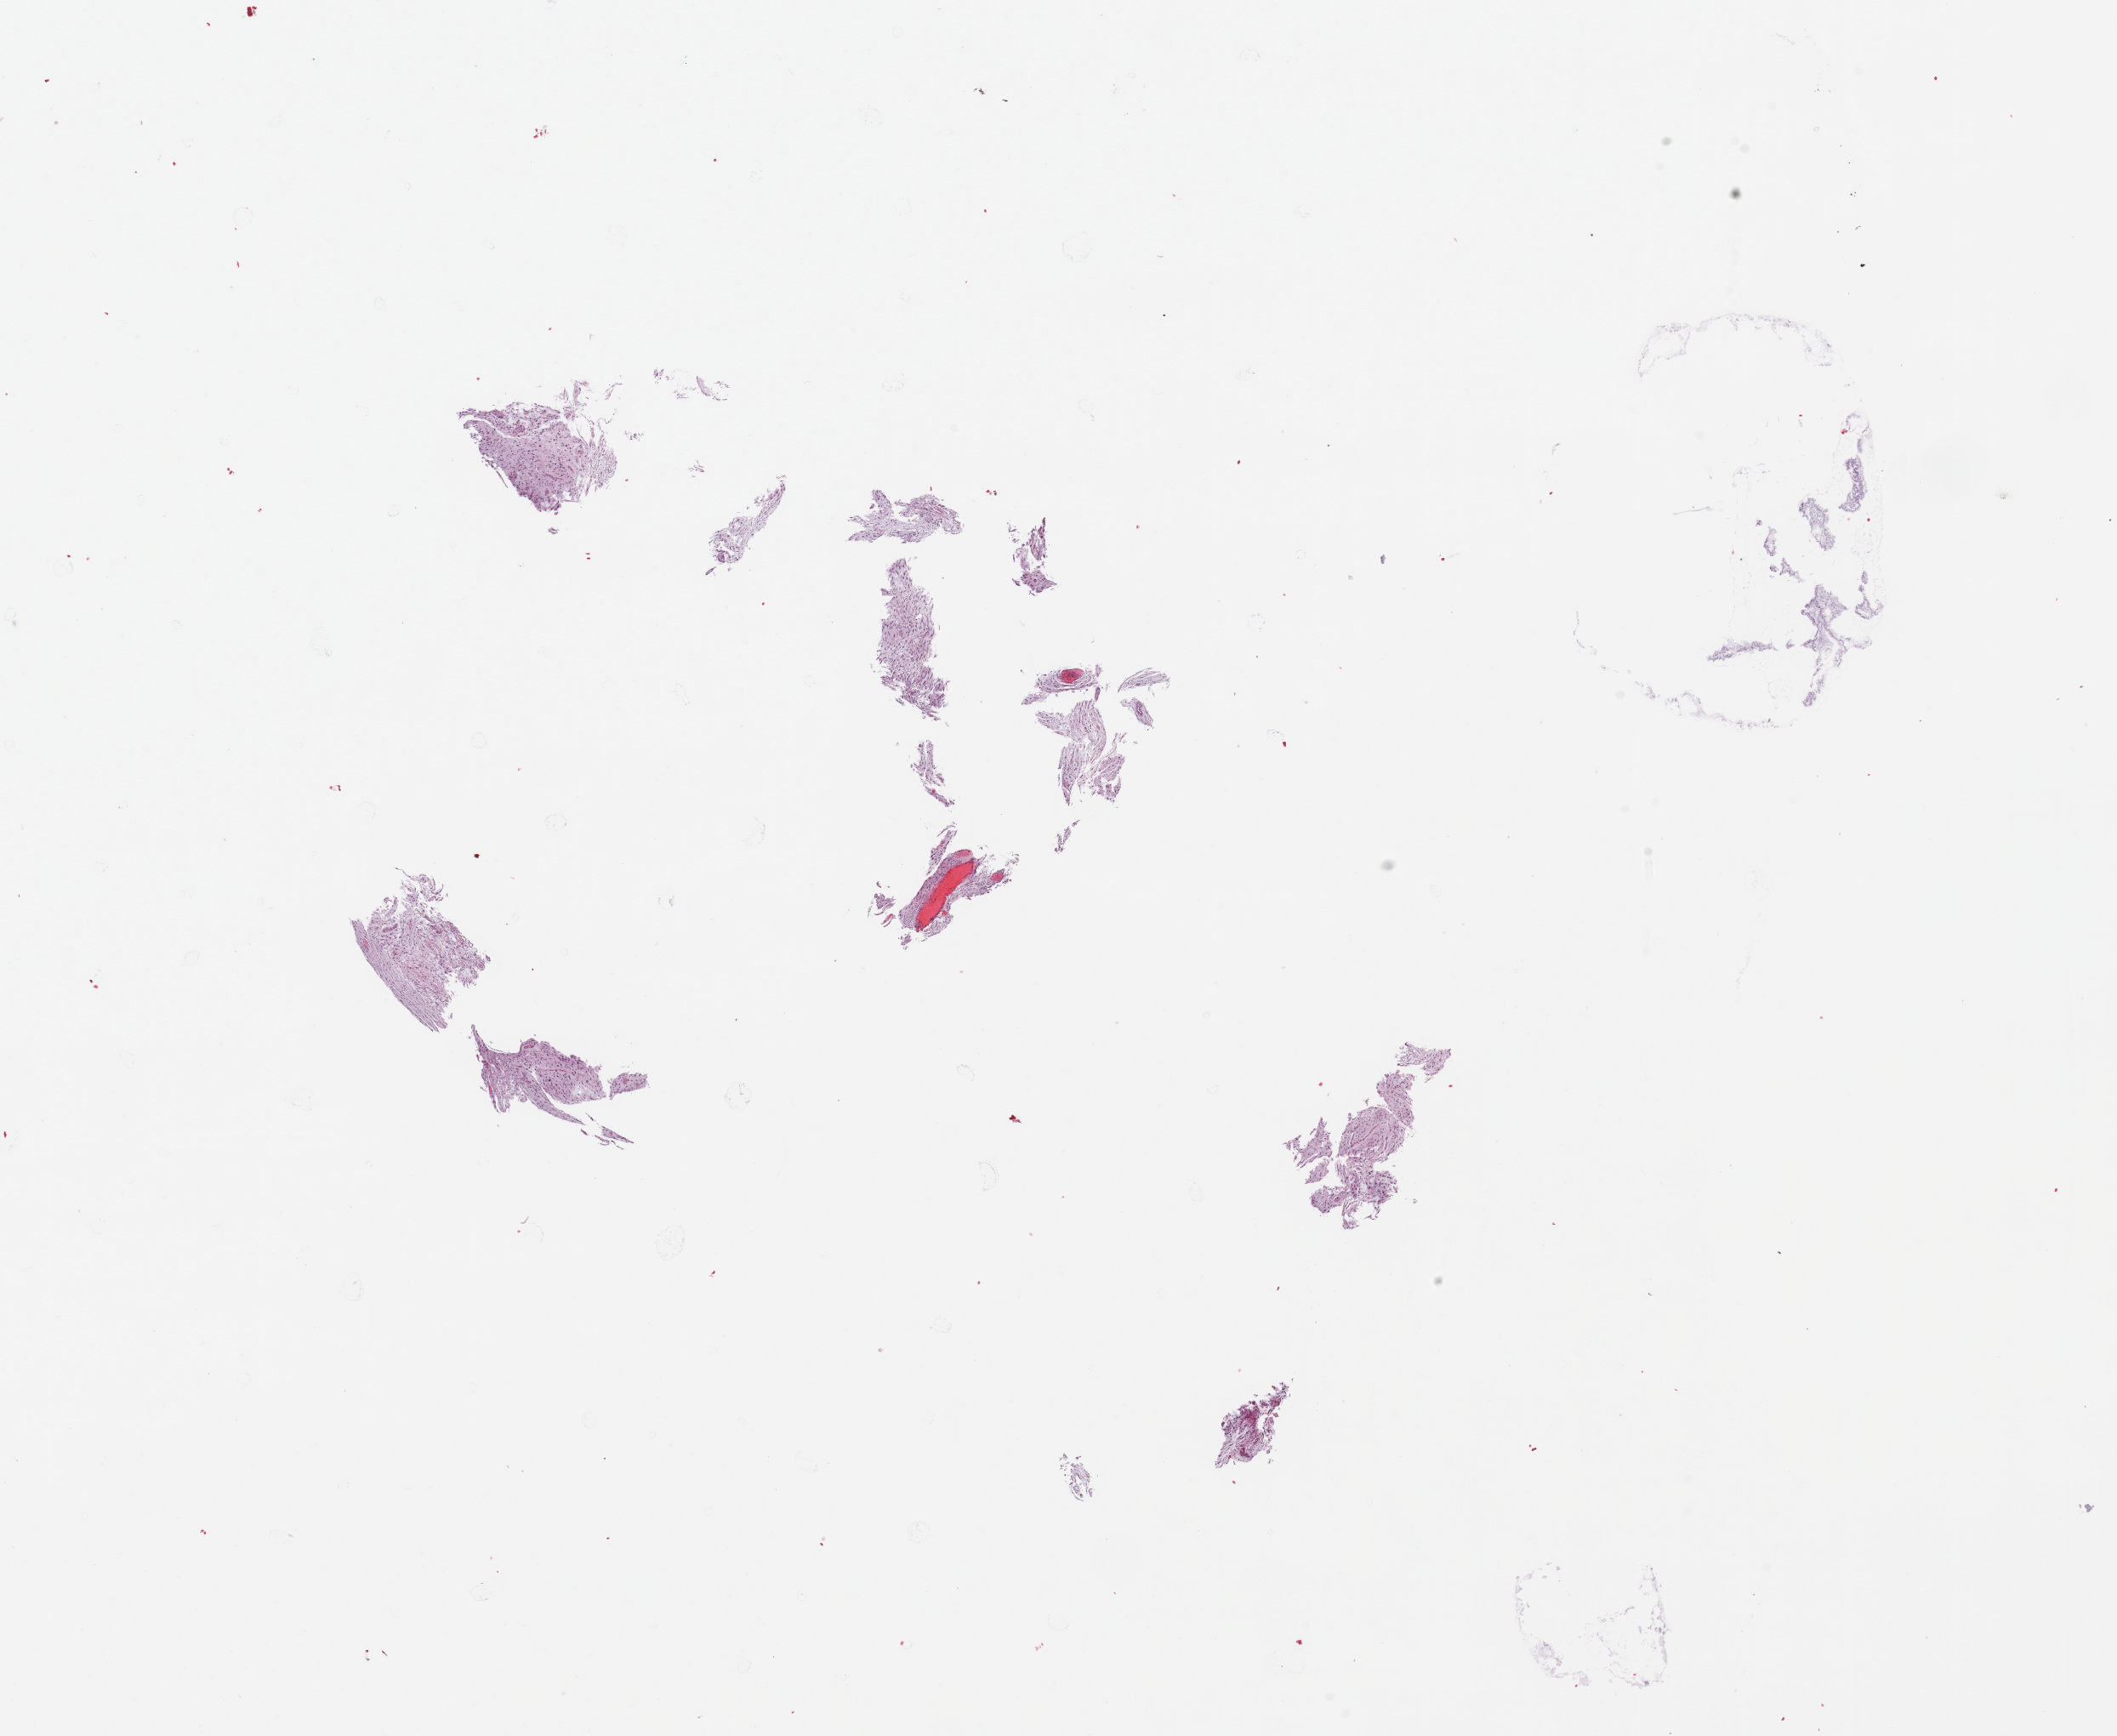
Whole-slide histology image, H&E-stained, shown as a low-resolution overview of the whole scanned area (about 19.7 x 16.1 mm, slide scanned at 20x), tumour tissue sample, sampled site: frontal lobe. Female, 57 y/o.
Diagnosis: Glioblastoma.